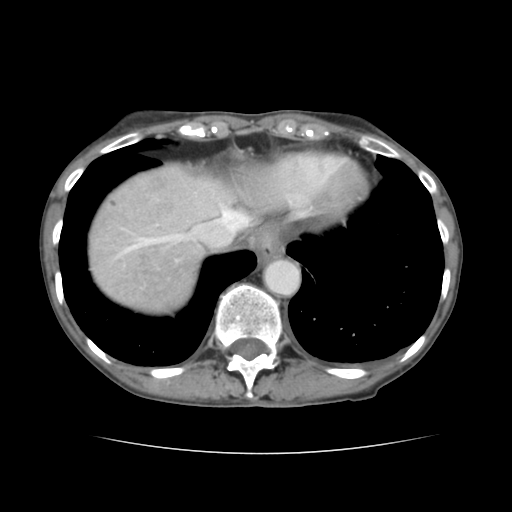
Contrast-enhanced abdominal CT, one axial slice. Position 125 of 136 along the scan axis. 120 kVp. Intravenous contrast given. Soft-tissue window (W 400 / L 40 HU). 512 × 512 image matrix, field of view 319 × 319 mm. Female patient, age 77 years. Case-level facts recorded for this patient, not image findings: diagnosis: colorectal cancer liver metastases, imaged before liver resection; multiple liver metastases: yes; largest metastasis: 3 cm; disease in both lobes: no.
Structures marked on this image (outlined manually by an expert reader):
- hepatic veins: box from (x=117, y=198) to (x=249, y=257) px
- liver: (x=88, y=164)–(x=247, y=312)
- planned liver remnant (the part of the liver to remain after resection): (x=191, y=175)–(x=254, y=217)